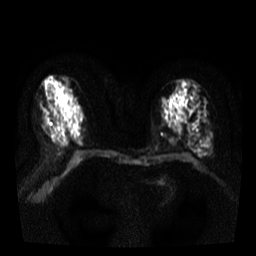
Breast MRI, one axial slice; slice 18 of 38 in the series (ordered by position); diffusion-weighted series; image 2 of 4 stored at this slice position (different b-values; order by instance number); 3 T; 5 mm slice thickness; 256 × 256 image matrix, field of view 320 × 320 mm. Female patient.
Annotated regions visible in this slice (manually delineated by an expert):
- tumour on diffusion-weighted imaging: bounding box <196,150,201,157> (left, top, right, bottom; pixels)